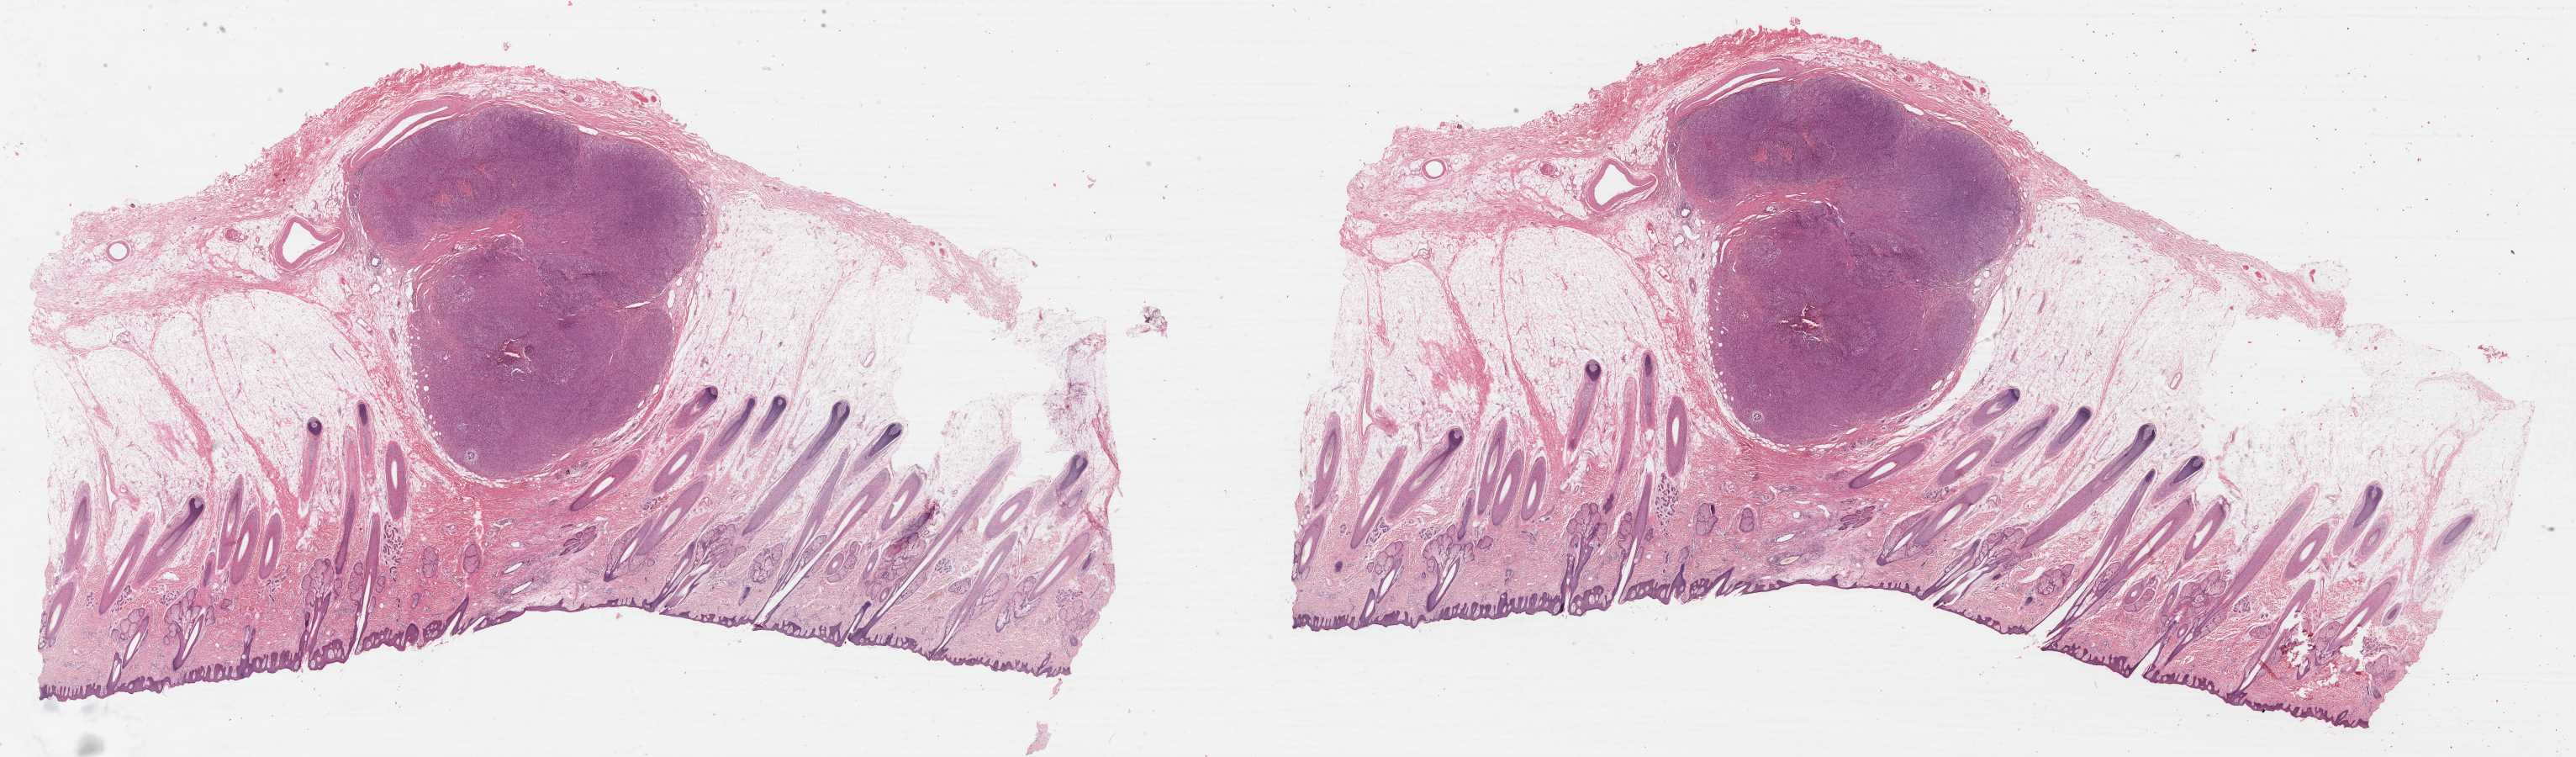
H&E whole-slide image — shown as a low-resolution overview of the whole scanned area (about 48.2 x 14.1 mm). Formalin-fixed paraffin-embedded (FFPE) diagnostic section. Metastatic tumour sample, sampled site not recorded. Patient: male, age at initial diagnosis 19 years.
• this section: metastatic tumour tissue
• patient diagnosis: Malignant melanoma, NOS